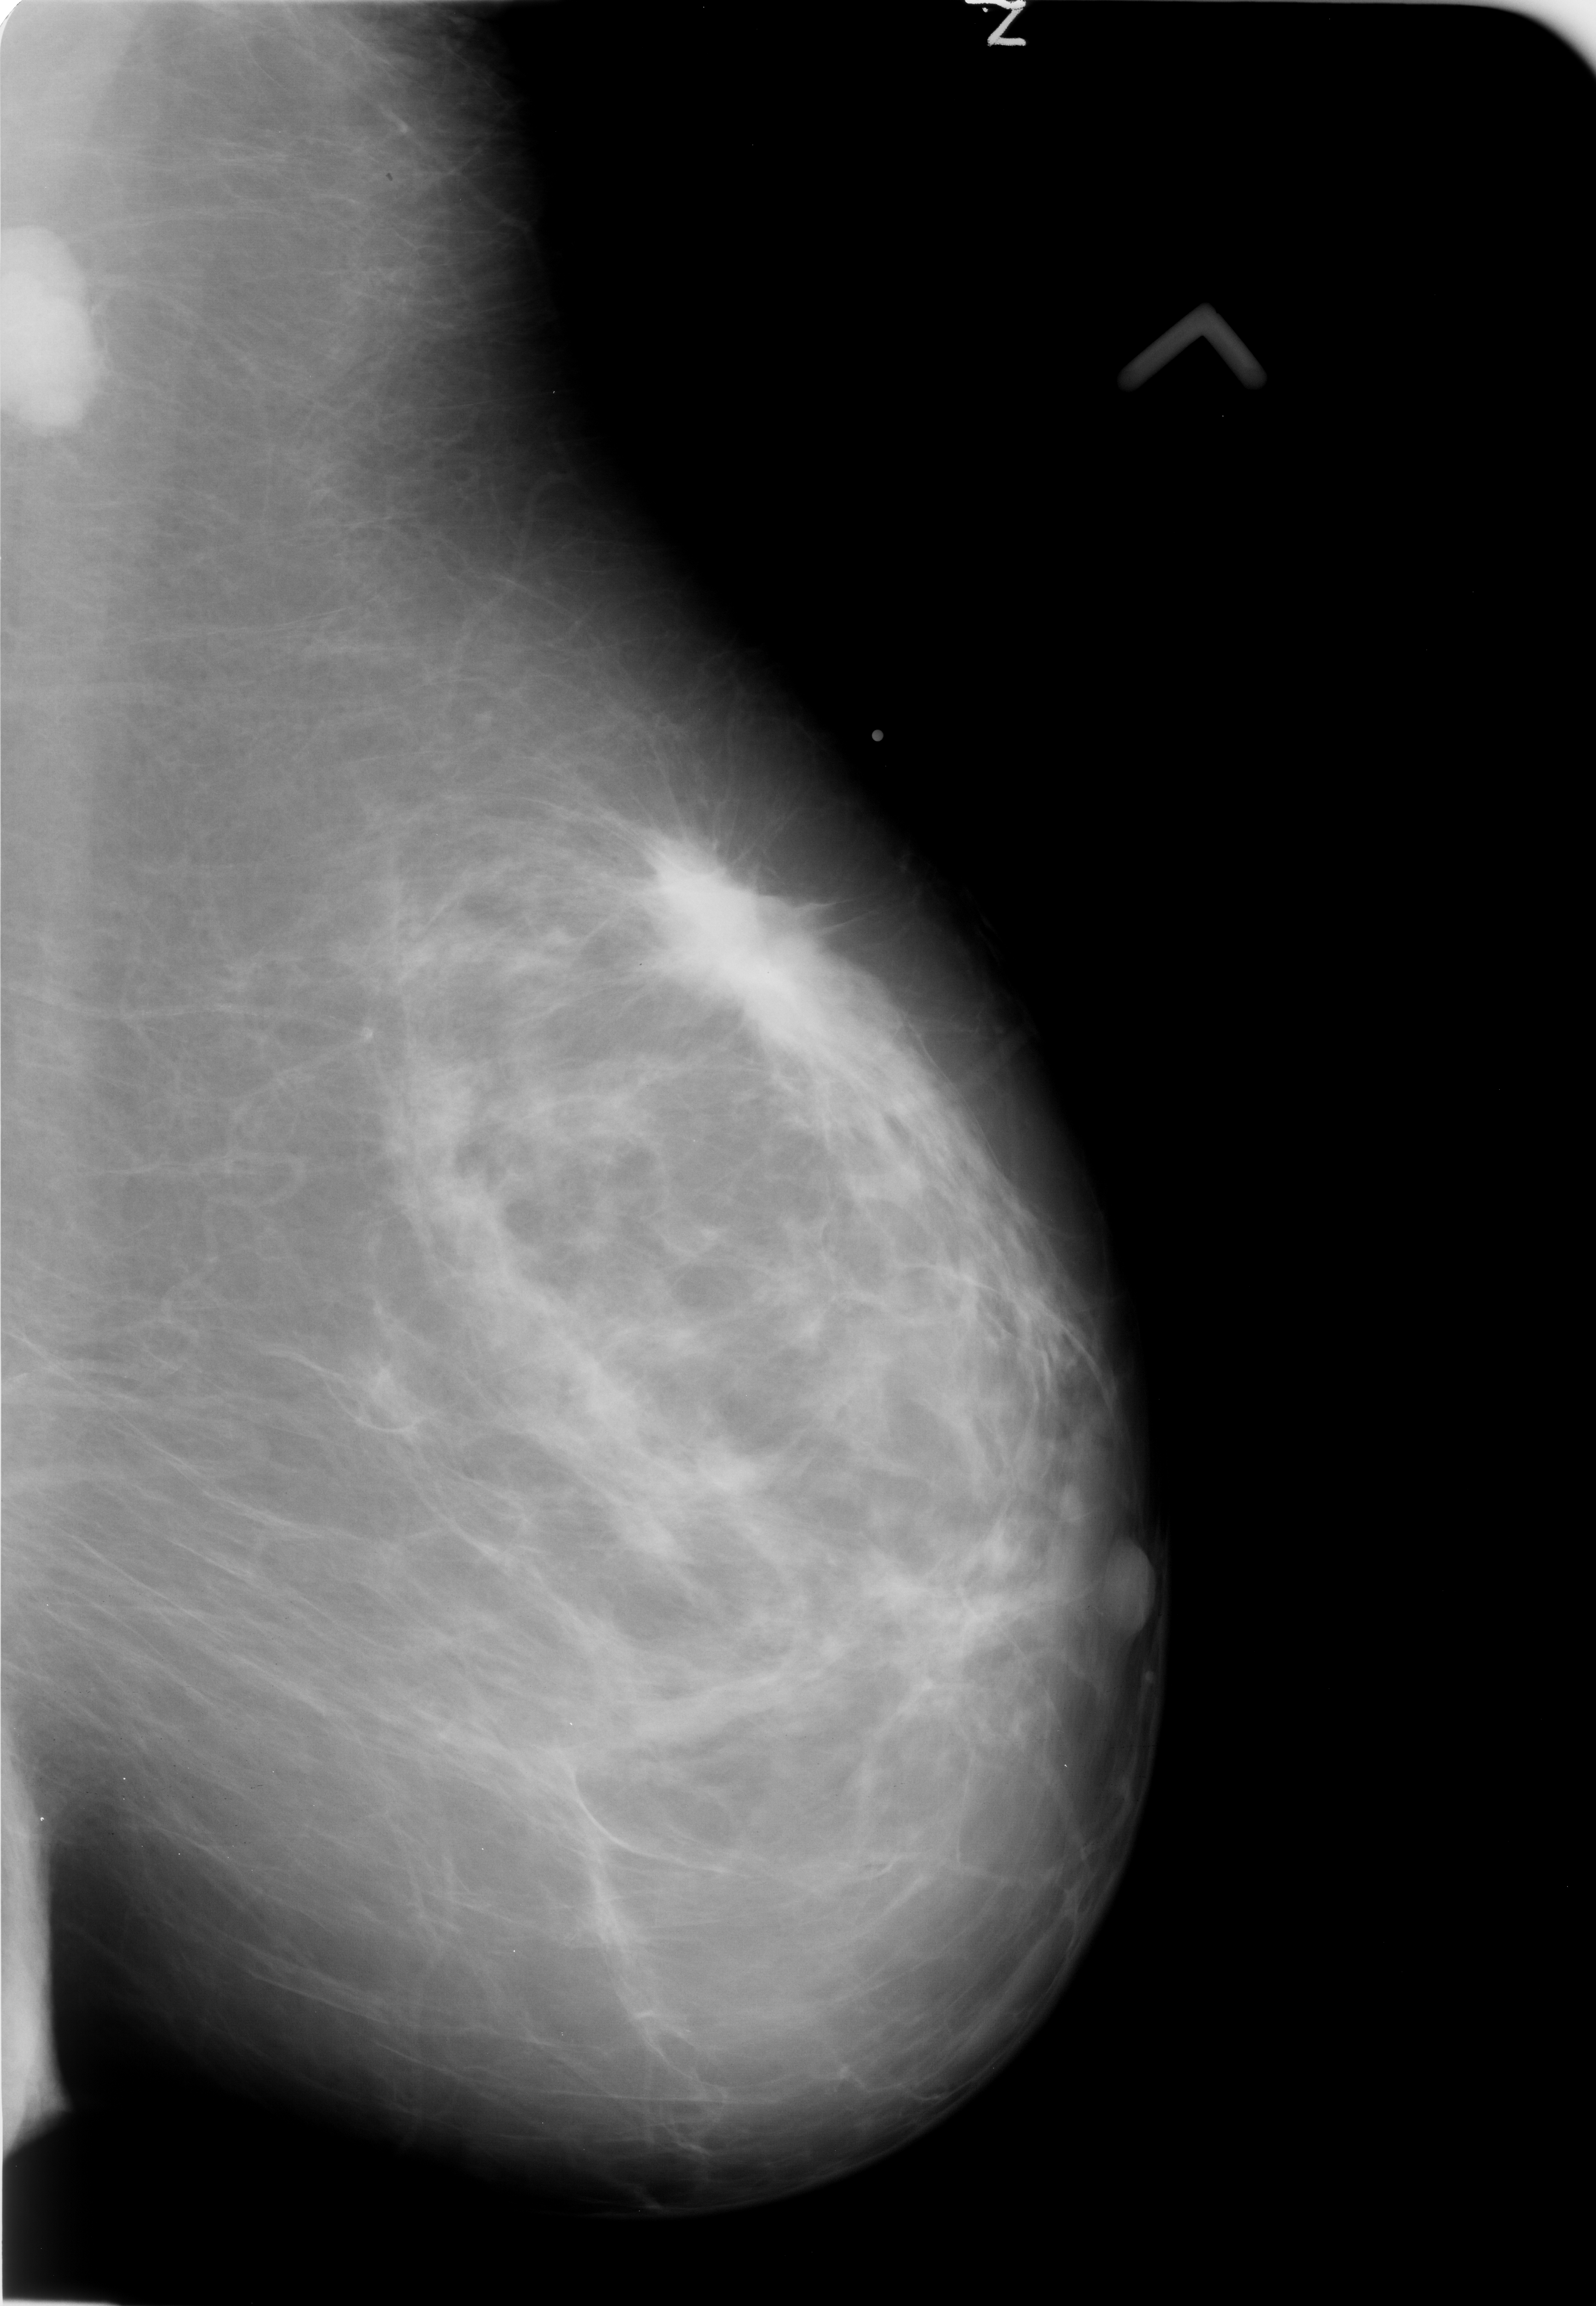
Mammogram (digitized film); left breast; MLO view; breast composition: scattered fibroglandular densities (BI-RADS density category 2 of 4); 1596 × 2306 image matrix.
Expert-marked regions of interest on this image (one box per marked abnormality):
- mass, shape irregular / architectural distortion, margins spiculated; BI-RADS assessment category 5; subtlety rating 5 on a 1 (subtle) to 5 (obvious) scale; pathology (as recorded): malignant: bounding box [x1, y1, x2, y2] px = [621, 825, 867, 1051]